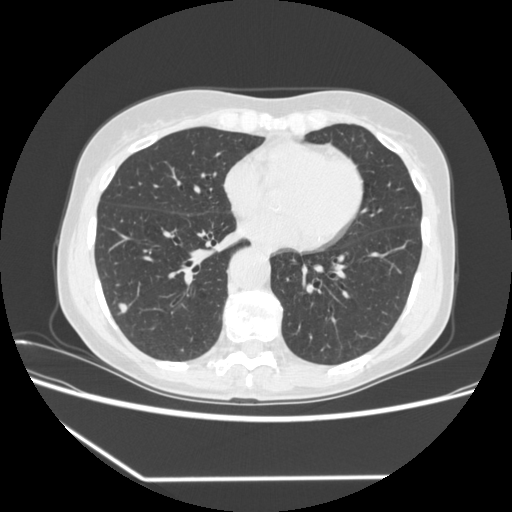
Low-dose screening chest CT, one axial slice; position 154 of 323 along the scan axis; 120 kVp; lung window (W 1500 / L -600 HU); 1.25 mm slice thickness; 512 × 512 image matrix, field of view 360 × 360 mm.
Outlined on this slice (manually delineated by an expert):
- lesion 2 (nodule, lower lobe of right lung): box from (x=119, y=303) to (x=128, y=314) px